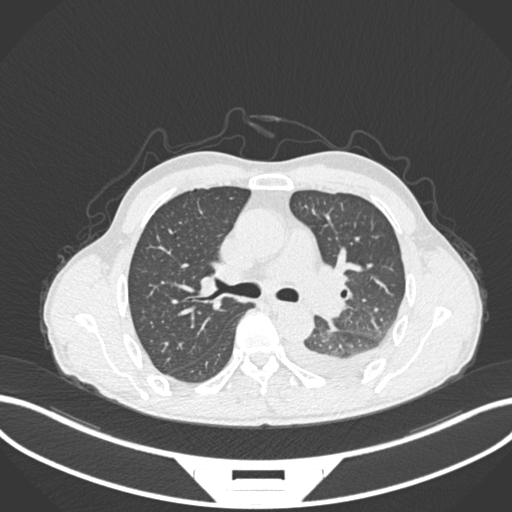
Chest CT, one axial slice; position 159 of 222 along the scan axis; reconstruction kernel B30f; 120 kVp; lung window (W 1500 / L -600 HU); 1 mm slice thickness; 512 × 512 image matrix. Male patient, age 47 years. From the clinical record (not read from this slice): clinical TNM (as recorded): T3 N1 M1c; histopathological grade: G3.
Outlined on this slice (bounding box drawn by a radiologist):
- lung tumour (recorded histology: small cell carcinoma): box from (x=315, y=291) to (x=346, y=323) px